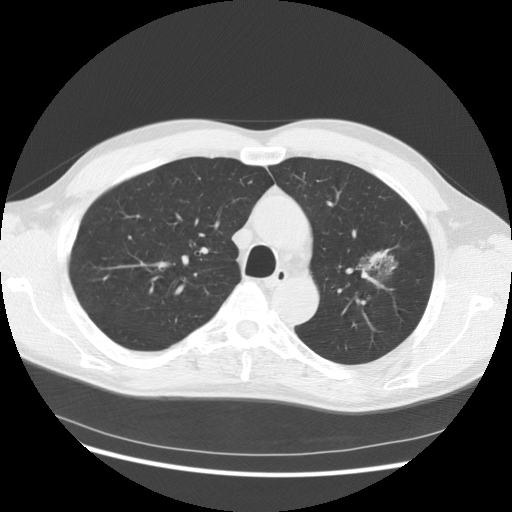
Low-dose screening chest CT, one axial slice. Position 100 of 145 along the scan axis. Lung window (W 1500 / L -600 HU). 2.5 mm slice thickness. 512 × 512 image matrix.
Annotated regions visible in this slice (outlined manually by an expert reader):
- lesion 1 (tumor, upper lobe of left lung): bounding box <370,250,387,267> (left, top, right, bottom; pixels)